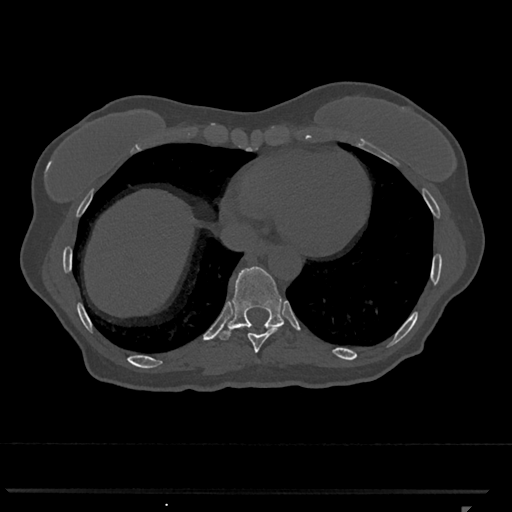
CT including the spine, one axial slice; position 591 of 793 along the scan axis; reconstruction kernel Br40s/3; 120 kVp; bone window (W 1800 / L 400 HU); 0.5 mm slice thickness; 512 × 512 image matrix. Patient: female, 62 years. From the clinical record (not read from this slice): primary cancer: renal.
Annotated regions visible in this slice (semi-automatically segmented with operator editing):
- T10 vertebra: box from (x=219, y=266) to (x=284, y=340) px
- T9 vertebra: (x=241, y=326)–(x=282, y=353)